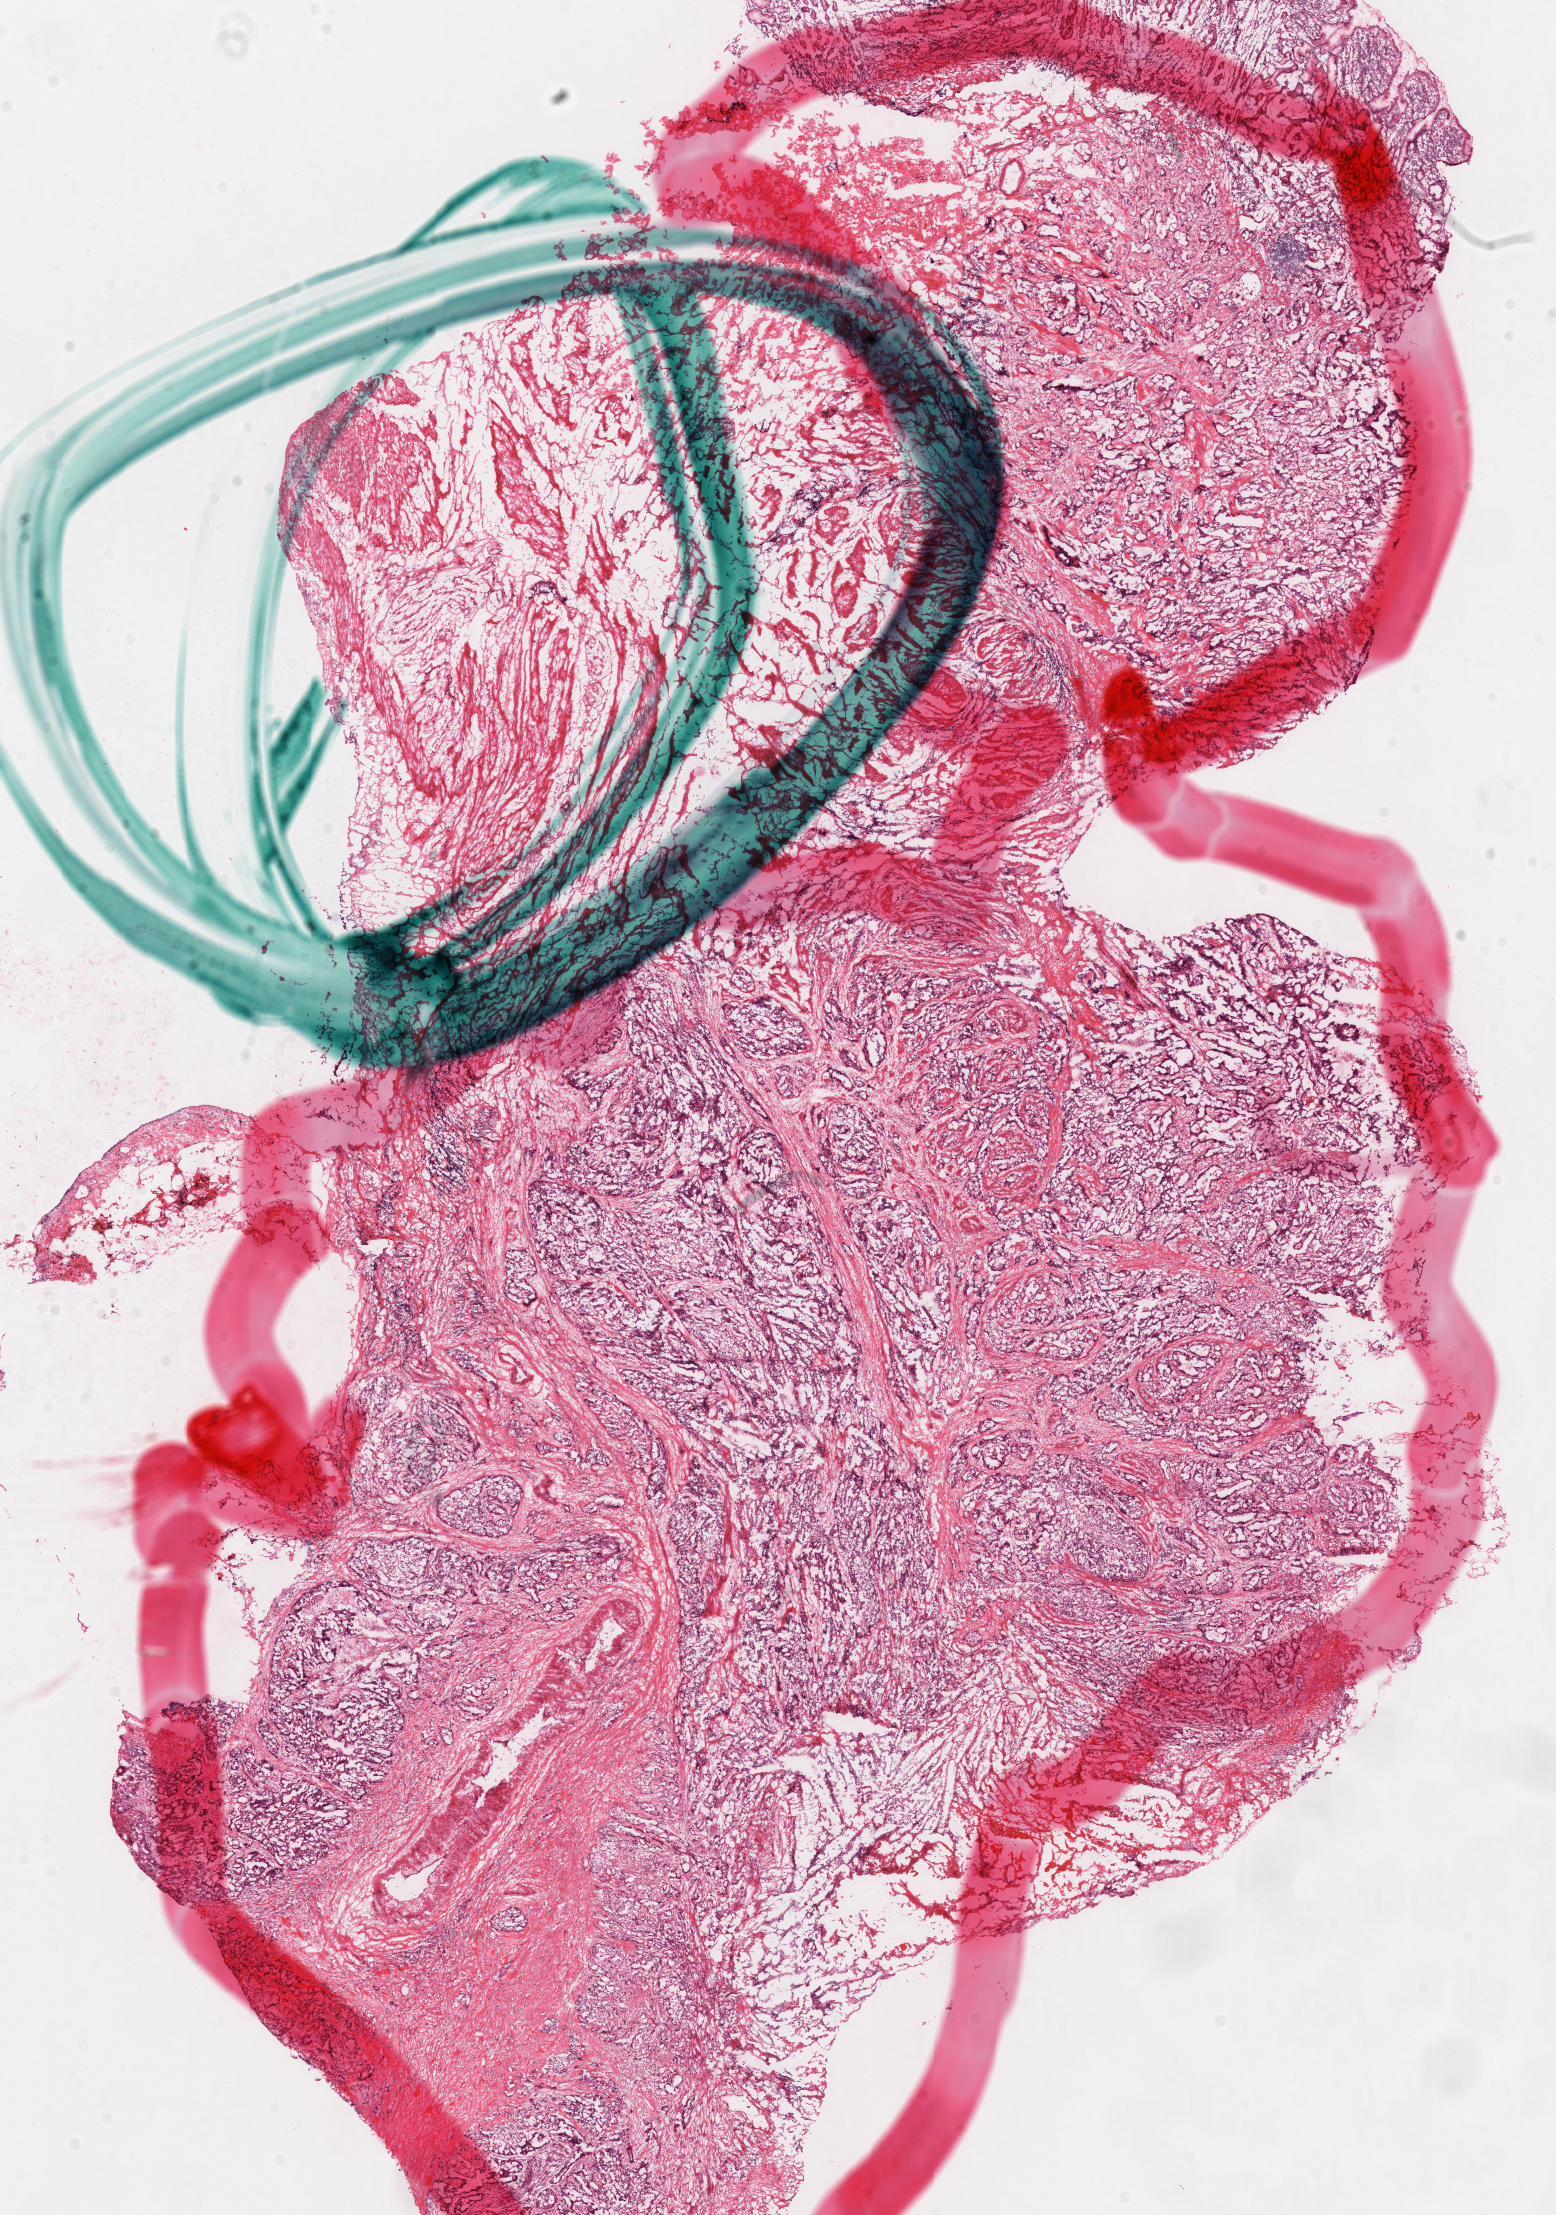
Whole-slide histology image, Hematoxylin and eosin (H&E) stained, whole scanned area (about 12.2 x 17.4 mm, slide scanned at 40x) shown as a low-resolution overview, frozen section from the top of the tissue portion, primary tumour sample from the stomach. Male, age 63 years at initial diagnosis. Histologic grade: G2 (moderately differentiated). Composition of this section per pathologist review: tumour cells 100%, tumour nuclei 70%, normal cells 0%, stromal cells 0%, necrosis 0%. Inflammatory infiltration, as recorded: lymphocyte infiltration 10%, monocyte infiltration 0%, neutrophil infiltration 5%.
Pathologic diagnosis: Adenocarcinoma, NOS. AJCC pathologic stage: IV (6th edition).